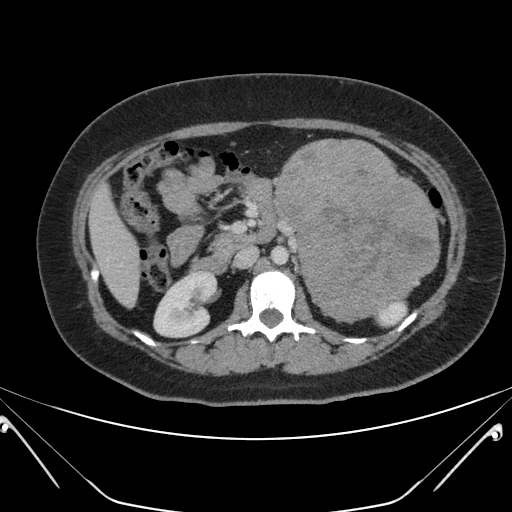
Contrast-enhanced abdominal CT, one axial slice; slice 111 of 168 in the series (ordered by position); intravenous contrast given; soft-tissue window (W 400 / L 40 HU); 3 mm slice thickness; 512 × 512 image matrix, field of view 394 × 394 mm. Female patient, age 26 years. Case-level facts recorded for this patient, not image findings: diagnosis: adrenocortical carcinoma; tumour side: left adrenal; tumour size at pathology: 28 cm.
Structures marked on this image (semi-automatically segmented with operator editing):
- mass: bounding box <275,138,439,322> (left, top, right, bottom; pixels)